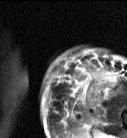
MRI of an extremity soft-tissue mass, one axial slice; slice 16 of 87 in the series (ordered by position); T2-weighted fat-saturated; MR volume resampled by the dataset authors to the PET/CT grid (not the native acquisition matrix); 3.27 mm slice thickness; 127 × 138 image matrix, field of view 124 × 135 mm. Female patient. Case-level facts recorded for this patient, not image findings: histological type: pleiomorphic leiomyosarcoma; grade: high; site of the primary tumour: left biceps.
Outlined on this slice (expert contour drawn on MRI and transferred to this co-registered scan by the dataset authors):
- gross tumour volume including surrounding oedema: bounding box (x1, y1, x2, y2) in pixels: (88, 73, 119, 102)
- gross tumour volume (mass): (93, 73, 105, 83)